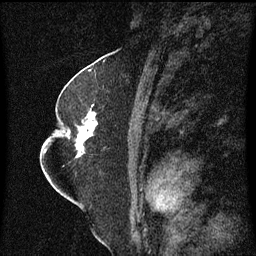
Breast MRI (dynamic contrast-enhanced), one sagittal slice. Position 34 of 60 along the scan axis. Dynamic contrast-enhanced series, image 2 of 3 at this slice position (ordered by acquisition). 1.5 T. TE 4.2 ms, TR 8.4 ms. 2 mm slice thickness. 256 × 256 image matrix, field of view 200 × 200 mm. Patient: female, 52 years. From the clinical record (not read from this slice): setting: breast cancer imaged before/during neoadjuvant chemotherapy; receptor status: HR-positive, HER2-negative.
Structures marked on this image (semi-automatically segmented with operator editing):
- analysis volume of interest (the breast-tissue region the enhancement analysis was run in; not a lesion): bounding box <64,104,99,159> (left, top, right, bottom; pixels)
- tumour enhancement mask (voxels above the 70 % enhancement threshold inside the analysis volume of interest): <69,112,98,157>